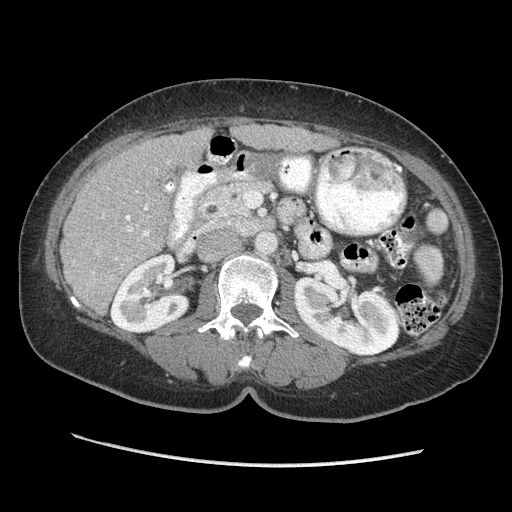
Contrast-enhanced abdominal CT (liver protocol), one axial slice; slice 113 of 170 in the series (ordered by position); reconstruction kernel STANDARD; 140 kVp; soft-tissue window (W 400 / L 40 HU); 2.5 mm slice thickness; 512 × 512 image matrix. Case-level facts recorded for this patient, not image findings: diagnosis: hepatocellular carcinoma (patient treated with transarterial chemoembolisation; whether this scan precedes or follows treatment is not stated here); TNM stage (as recorded): Stage-II; Child-Pugh class: A; tumour differentiation: no biopsy; tumour nodularity: multinodular.
Outlined on this slice (semi-automatically segmented with operator editing):
- liver parenchyma outside the tumour (the mass and vessels are separate outlines, so this box may not span the whole liver): bounding box <60,124,334,314> (left, top, right, bottom; pixels)
- liver vessels: <92,162,170,274>